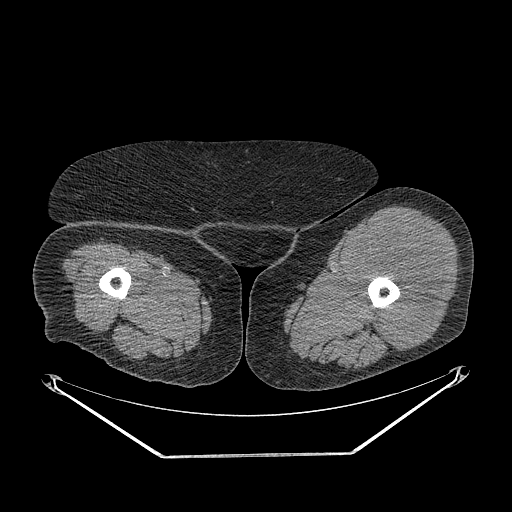
CT of an extremity soft-tissue mass (from a PET/CT study), one axial slice. 140 kVp. Soft-tissue window (W 400 / L 40 HU). 512 × 512 image matrix, field of view 500 × 500 mm. Female patient. Case-level facts recorded for this patient, not image findings: histological type: undifferentiated – high grade; grade: high; site of the primary tumour: left thigh.
Structures marked on this image (expert contour drawn on MRI and transferred to this co-registered scan by the dataset authors):
- gross tumour volume including surrounding oedema: box from (x=352, y=221) to (x=446, y=350) px
- gross tumour volume (mass): (x=352, y=221)–(x=446, y=350)